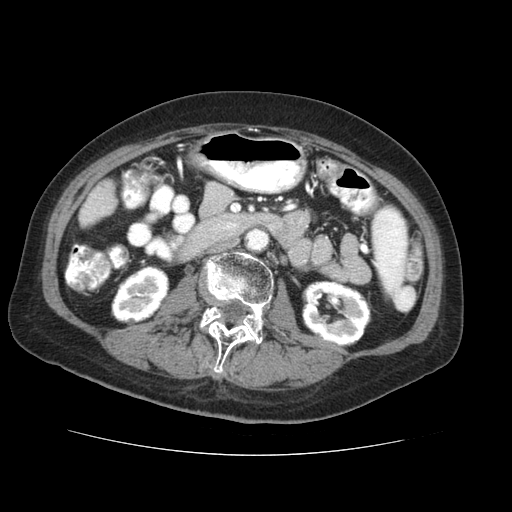
Contrast-enhanced abdominal CT (liver protocol), one axial slice. Slice 4 of 73 in the series (ordered by position). Reconstruction kernel STANDARD. Soft-tissue window (W 400 / L 40 HU). 512 × 512 image matrix, field of view 360 × 360 mm. From the clinical record (not read from this slice): diagnosis: hepatocellular carcinoma (patient treated with transarterial chemoembolisation; whether this scan precedes or follows treatment is not stated here); TNM stage (as recorded): Stage-IVB; Child-Pugh class: A.
Outlined on this slice (semi-automatically segmented with operator editing):
- liver parenchyma outside the tumour (the mass and vessels are separate outlines, so this box may not span the whole liver): bounding box <79,180,112,228> (left, top, right, bottom; pixels)